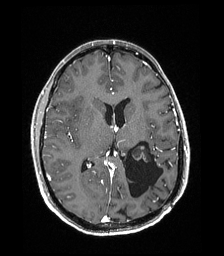
Brain MRI from a brain-tumour surgery series, one axial slice. Slice 91 of 192 in the series (ordered by position). T1-weighted post-contrast. 224 × 256 image matrix. Case-level facts recorded for this patient, not image findings: histopathology: Low grade glioma; IDH mutation: no; tumour location: Left Parieto-Occipital Intraventricular.
Structures marked on this image (outlined manually by an expert reader):
- previous resection cavity: bounding box [x1, y1, x2, y2] px = [125, 141, 163, 203]
- tumour: [132, 145, 148, 163]